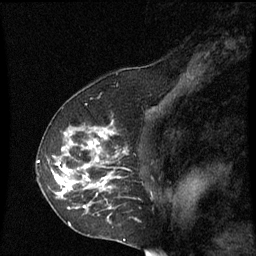
Breast MRI (dynamic contrast-enhanced), one sagittal slice; slice 41 of 60 in the series (ordered by position); dynamic contrast-enhanced series, image 2 of 3 at this slice position (ordered by acquisition); 1.5 T; TE 4.2 ms, TR 8.9 ms; 2 mm slice thickness; 256 × 256 image matrix. Female patient, age 53 years. From the clinical record (not read from this slice): setting: breast cancer imaged before/during neoadjuvant chemotherapy; receptor status: HR-positive, HER2-negative.
Structures marked on this image (semi-automatic segmentation, software-assisted and operator-edited):
- analysis volume of interest (the breast-tissue region the enhancement analysis was run in; not a lesion): bounding box <38,128,127,231> (left, top, right, bottom; pixels)
- tumour enhancement mask (voxels above the 70 % enhancement threshold inside the analysis volume of interest): <54,128,115,209>